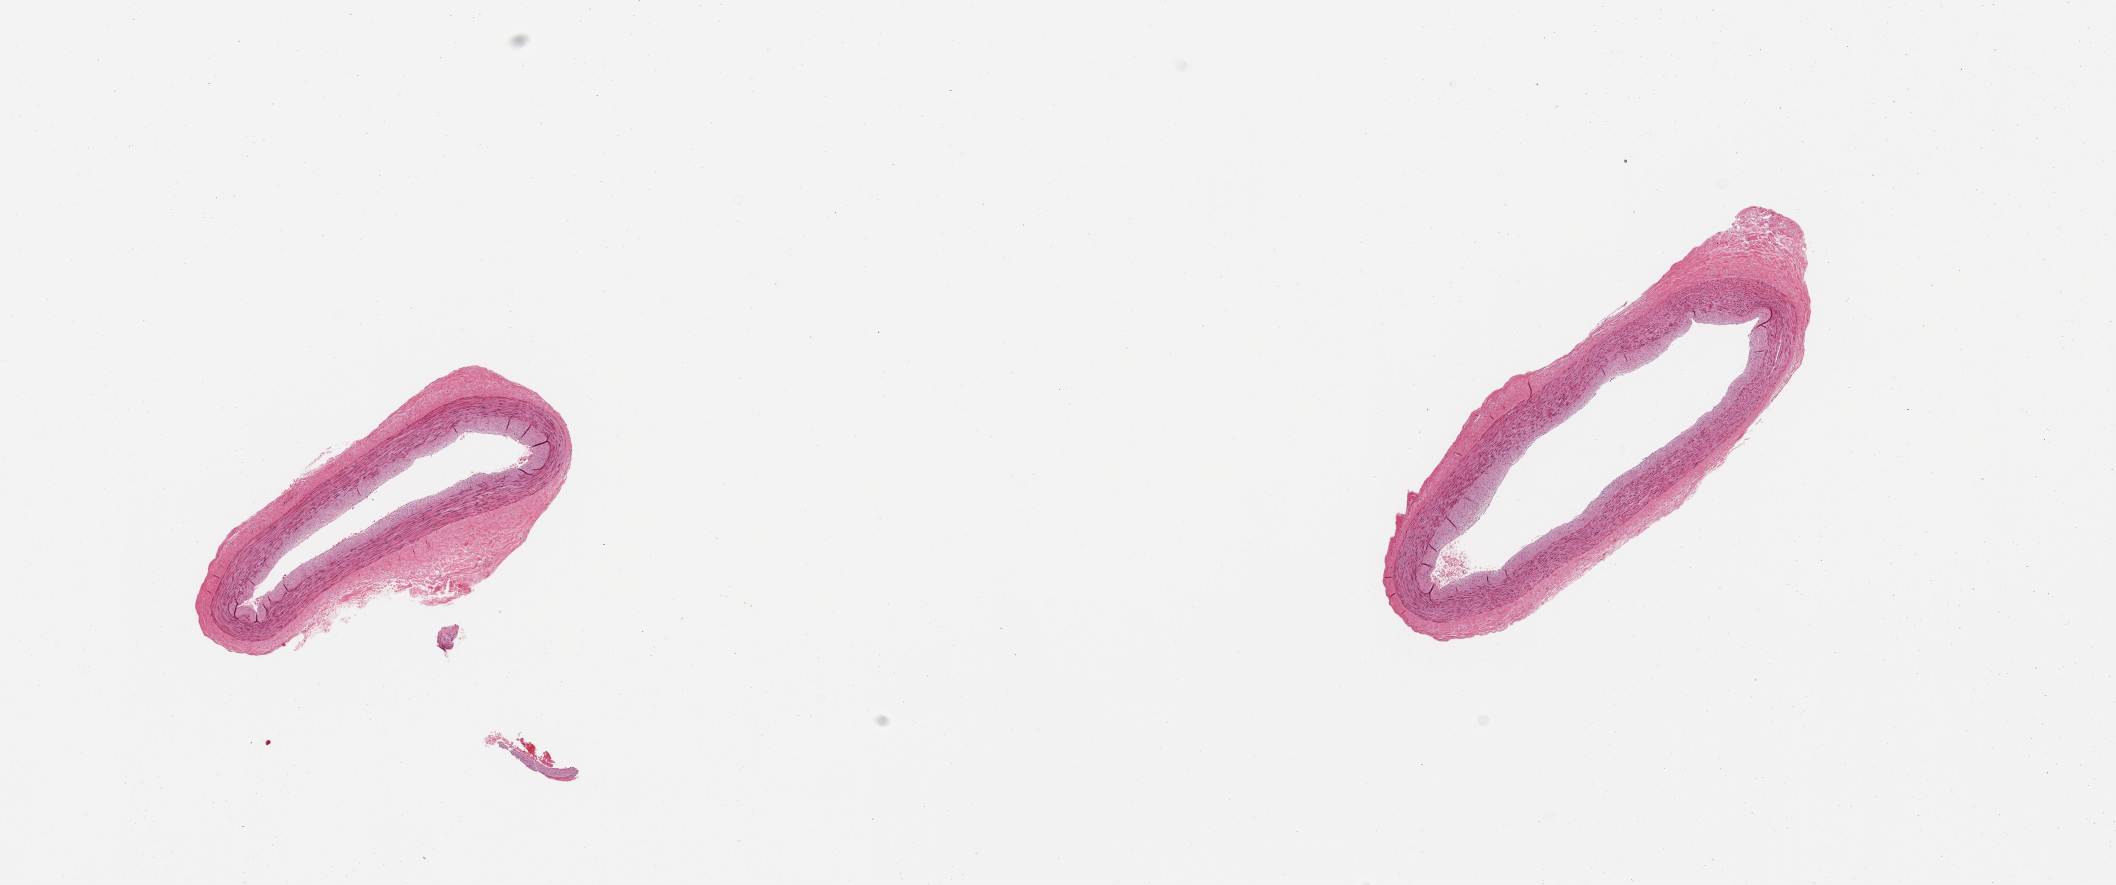
Digitized haematoxylin and eosin-stained section, brightfield — a low-resolution overview of the entire scanned area, about 16.7 x 7.0 mm (slide scanned at 20x); PAXgene-fixed paraffin-embedded (PFPE) section; section of tibial artery (target tissue); donor tissue sample. Male donor.
Review note (as recorded): 2 pieces; circumferential flat atherosclerotic plaque with insignificant luminal compromise; lumen open; >0.5 mm attached adventitia.